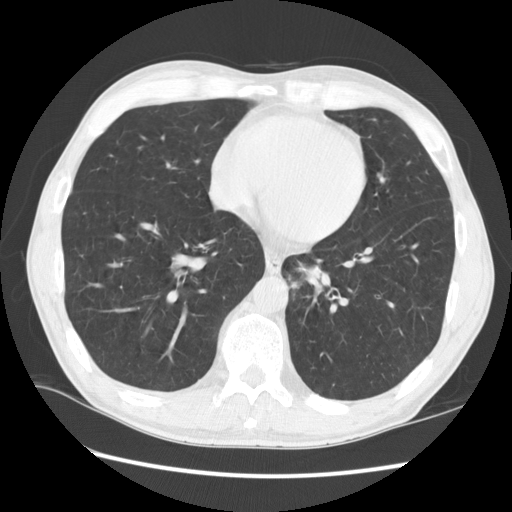
Low-dose screening chest CT, one axial slice; position 47 of 141 along the scan axis; reconstruction kernel STANDARD; 120 kVp; lung window (W 1500 / L -600 HU); 2.5 mm slice thickness; 512 × 512 image matrix, field of view 360 × 360 mm.
Annotated regions visible in this slice (manually delineated by an expert):
- lesion 2 (nodule, lower lobe of left lung): bounding box [x1, y1, x2, y2] px = [305, 269, 322, 288]